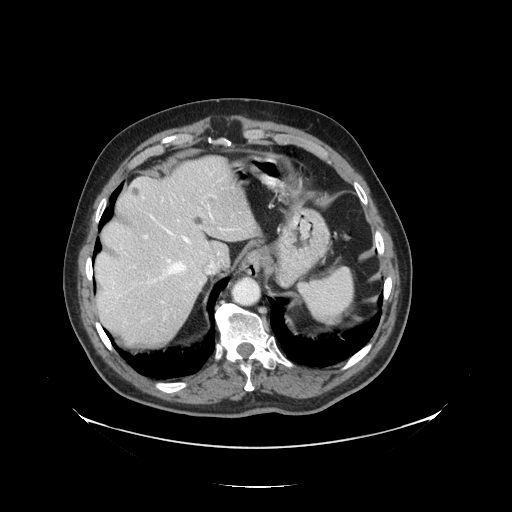
Contrast-enhanced abdominal CT, one axial slice. Slice 107 of 138 in the series (ordered by position). Reconstruction kernel STANDARD. Intravenous contrast given. Soft-tissue window (W 400 / L 40 HU). 2.5 mm slice thickness. 512 × 512 image matrix, field of view 497 × 497 mm. Male patient, age 77 years. Case-level facts recorded for this patient, not image findings: diagnosis: colorectal cancer liver metastases, imaged before liver resection; multiple liver metastases: no; largest metastasis: 1.5 cm.
Outlined on this slice (expert manual segmentation):
- hepatic veins: bounding box <147,205,214,285> (left, top, right, bottom; pixels)
- liver: <97,158,255,349>
- planned liver remnant (the part of the liver to remain after resection): <96,159,256,290>
- portal vein (with intrahepatic branches): <133,189,240,304>
- liver metastasis: <194,216,204,226>
- liver metastasis: <132,187,140,197>